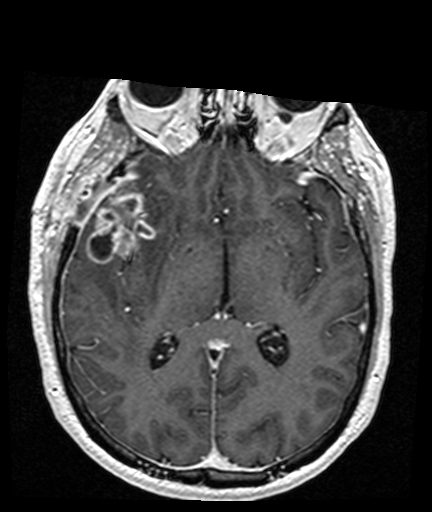
Brain MRI from a brain-tumour surgery series, one axial slice. Slice 89 of 176 in the series (ordered by position). T1-weighted post-contrast. 432 × 512 image matrix, field of view 194 × 230 mm. Case-level facts recorded for this patient, not image findings: histopathology: Glioblastoma; WHO grade: 4; IDH mutation: no.
Structures marked on this image (manually delineated by an expert):
- tumour: box from (x=86, y=188) to (x=156, y=264) px